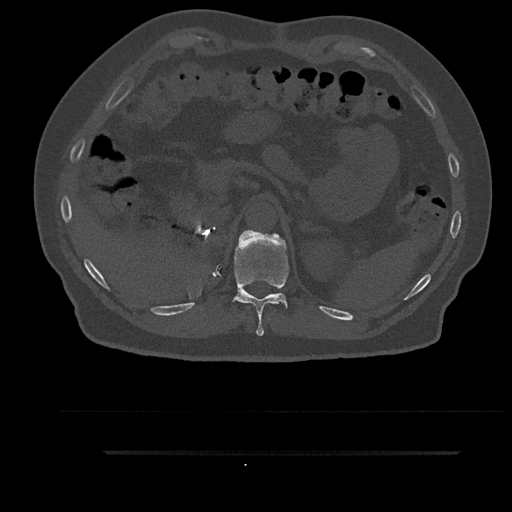
CT including the spine, one axial slice. Slice 296 of 797 in the series (ordered by position). Reconstruction kernel Br40s/3. Bone window (W 1800 / L 400 HU). 512 × 512 image matrix, field of view 432 × 432 mm. Patient: male, 63 years. From the clinical record (not read from this slice): primary cancer: renal.
Outlined on this slice (semi-automatic segmentation, software-assisted and operator-edited):
- T11 vertebra: bounding box [x1, y1, x2, y2] px = [226, 230, 290, 336]